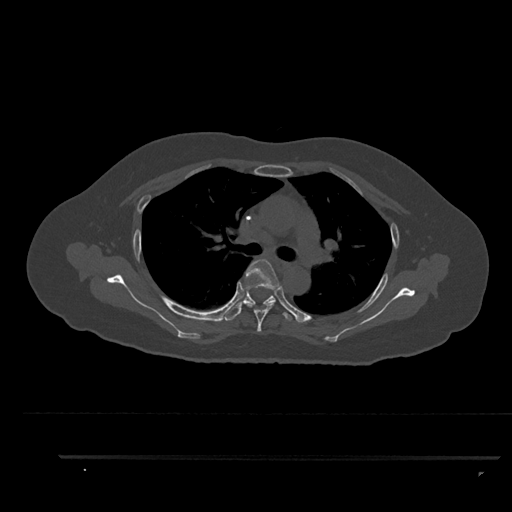
CT including the spine, one axial slice. Slice 623 of 797 in the series (ordered by position). Bone window (W 1800 / L 400 HU). 0.5 mm slice thickness. 512 × 512 image matrix. Female patient, age 44 years. Case-level facts recorded for this patient, not image findings: primary cancer: renal; vertebrae with lytic lesions (as recorded): L1.
Structures marked on this image (semi-automatic segmentation, software-assisted and operator-edited):
- T4 vertebra: bounding box <242,259,281,332> (left, top, right, bottom; pixels)
- T5 vertebra: <225,286,292,321>